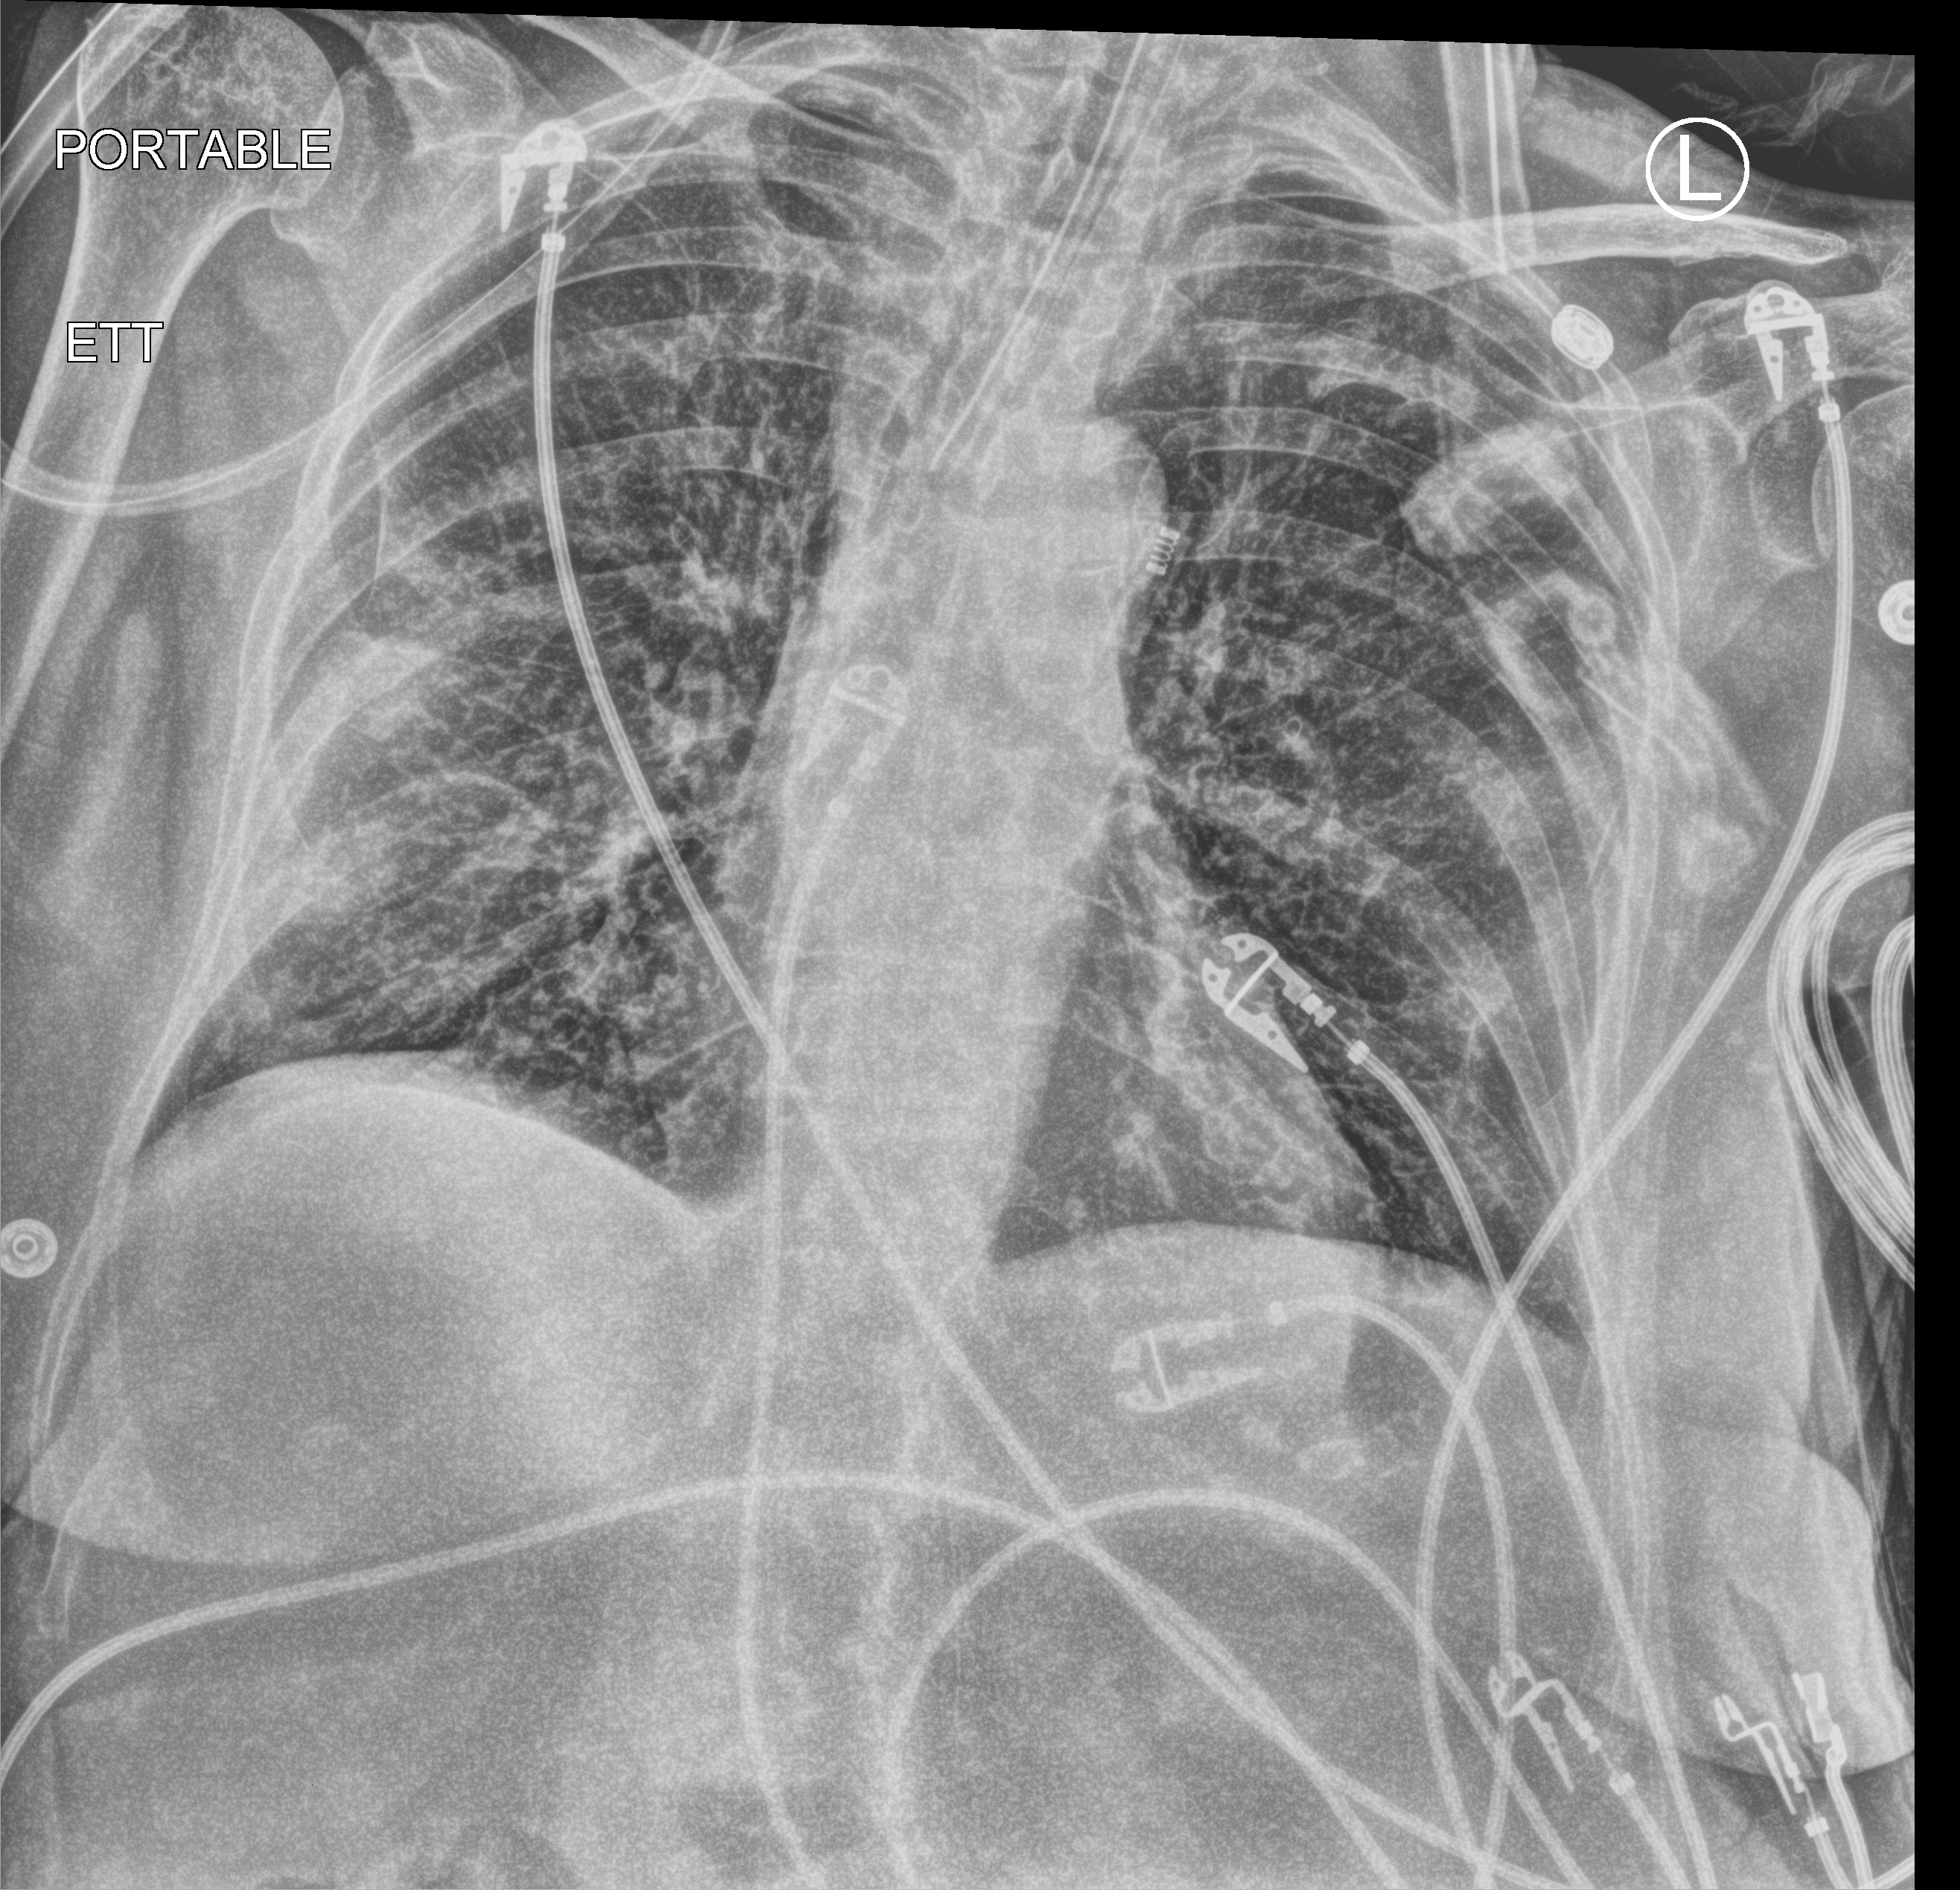
Portable chest radiograph; anteroposterior (AP) projection. Patient hospitalised with COVID-19; female, aged 75–90 years.
Hospital-stay facts (about this admission, not read from this image; timing relative to this image not recorded): diabetes (admission record): no; mechanically ventilated during this hospital stay: yes; admitted to intensive care during this hospital stay: yes.